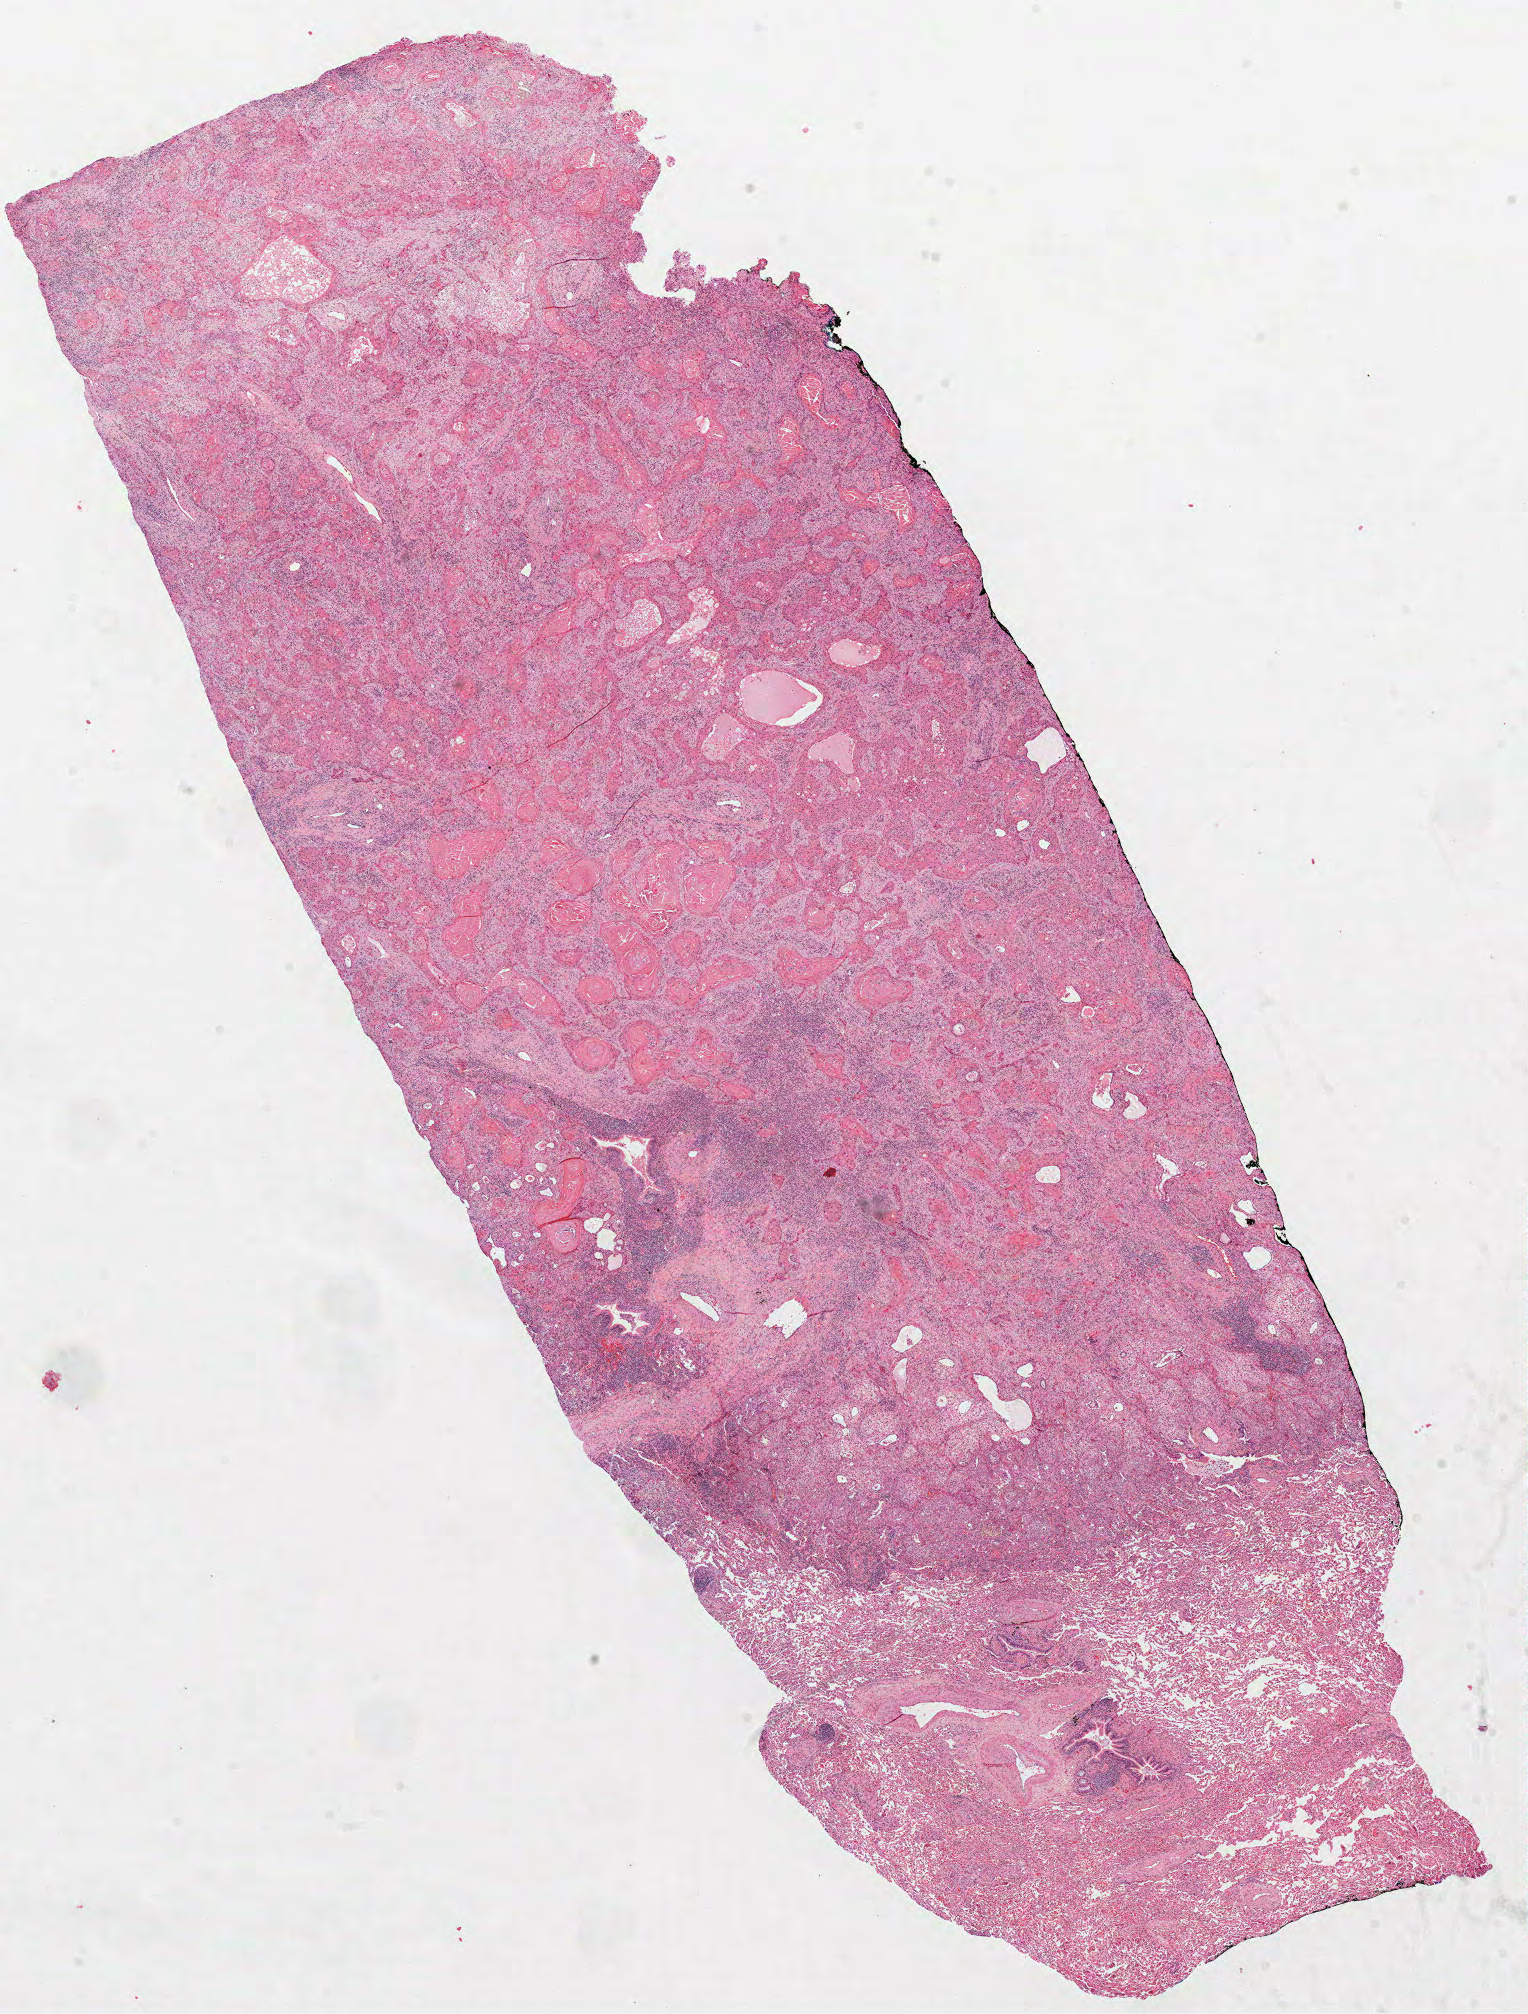
Digitized H&E-stained tissue section (whole slide), shown as a low-resolution overview of the whole scanned area (about 12.3 x 16.2 mm, acquisition: 40x scan); formalin-fixed paraffin-embedded (FFPE) diagnostic section; sample: primary tumour, lung. Male patient; age at initial diagnosis 68 years.
Diagnosis: Squamous cell carcinoma, NOS (lower lobe, lung).